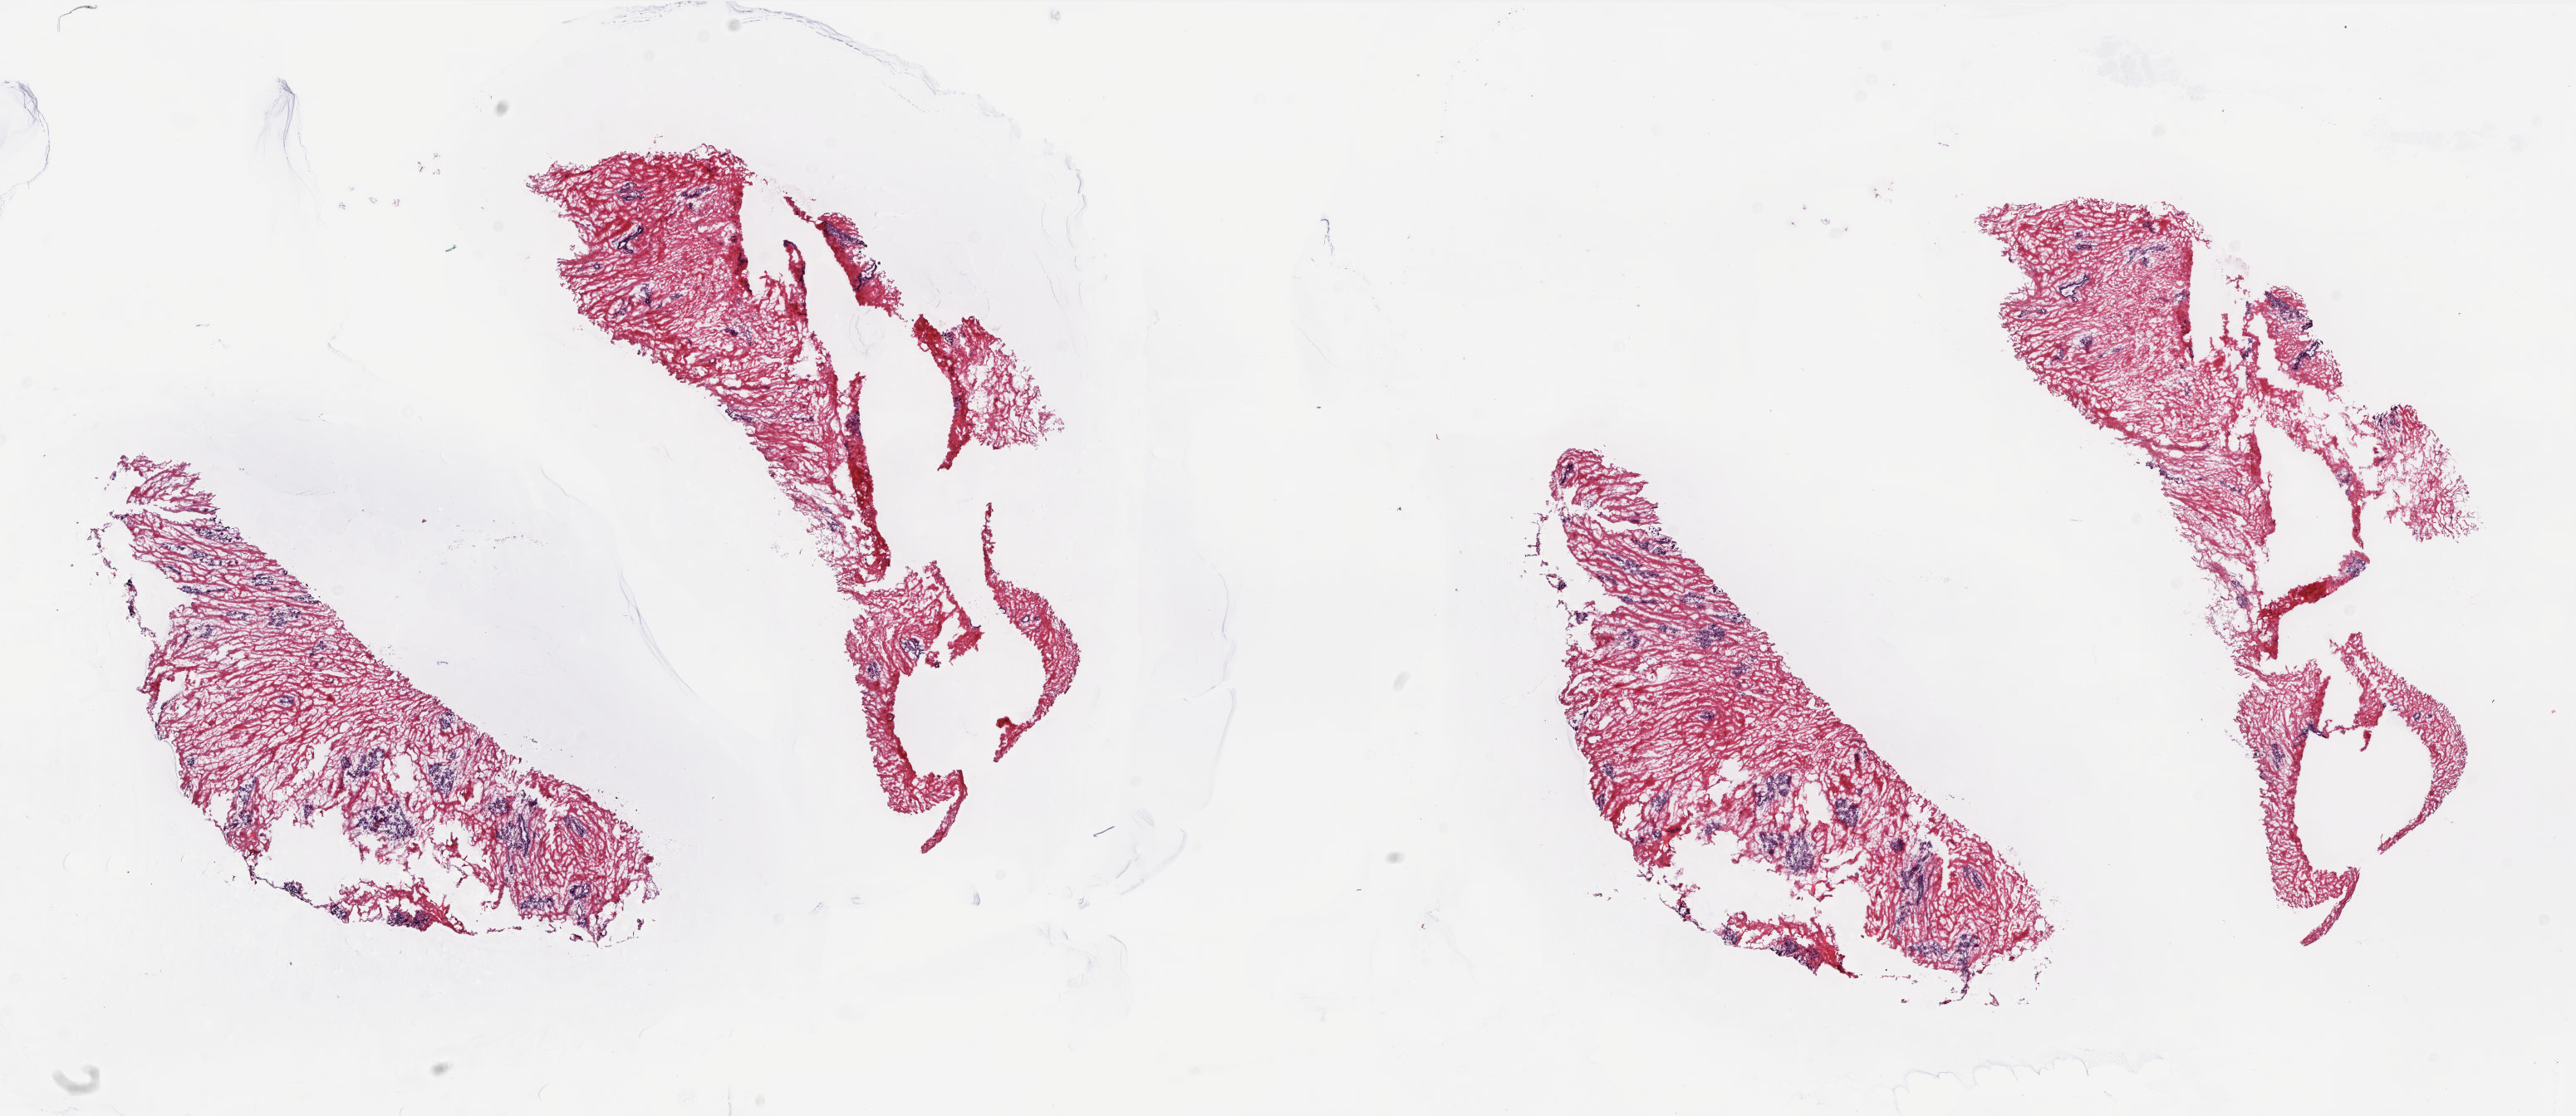
Whole-slide histology image, H&E-stained — whole scanned area (about 25.0 x 10.8 mm) shown as a low-resolution overview, frozen section from the top of the tissue portion, breast, solid tissue normal (non-tumour tissue) sample. Patient: female, age at initial diagnosis 40 years. Composition of this section per pathologist review: tumour cells 0%, tumour nuclei 0%, normal cells 20%, stromal cells 80%, necrosis 0%. Infiltration values recorded for this section: lymphocyte infiltration 2%, monocyte infiltration 0%, neutrophil infiltration 0%.
This section: solid tissue normal sample (biorepository sample class). Patient diagnosis: Lobular carcinoma, NOS.